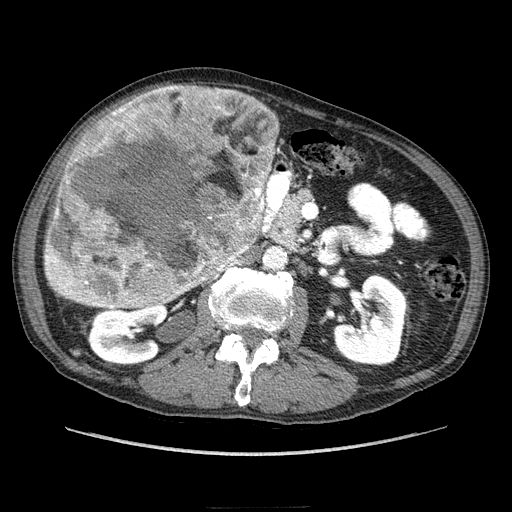
Contrast-enhanced abdominal CT (liver protocol), one axial slice. Position 101 of 218 along the scan axis. Soft-tissue window (W 400 / L 40 HU). 2.5 mm slice thickness. 512 × 512 image matrix. From the clinical record (not read from this slice): diagnosis: hepatocellular carcinoma (patient treated with transarterial chemoembolisation; whether this scan precedes or follows treatment is not stated here); TNM stage (as recorded): Stage-IIIA; Child-Pugh class: A; tumour differentiation: well differentiated; tumour nodularity: multinodular.
Outlined on this slice (semi-automatically segmented with operator editing):
- liver parenchyma outside the tumour (the mass and vessels are separate outlines, so this box may not span the whole liver): bounding box <216,88,254,246> (left, top, right, bottom; pixels)
- mass: <40,85,276,312>